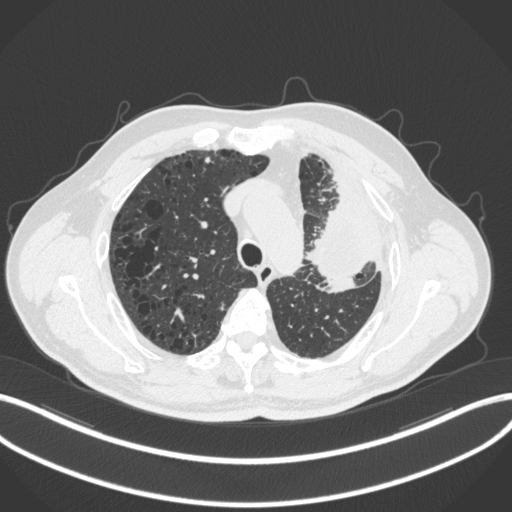
Chest CT, one axial slice; slice 228 of 286 in the series (ordered by position); reconstruction kernel B31f; lung window (W 1500 / L -600 HU); 1 mm slice thickness; 512 × 512 image matrix, field of view 400 × 400 mm. Patient: male, 68 years. Case-level facts recorded for this patient, not image findings: clinical TNM (as recorded): T3 N3 M1.
Outlined on this slice (bounding box drawn by a radiologist):
- lung tumour (recorded histology: adenocarcinoma): bounding box [x1, y1, x2, y2] px = [302, 193, 371, 293]